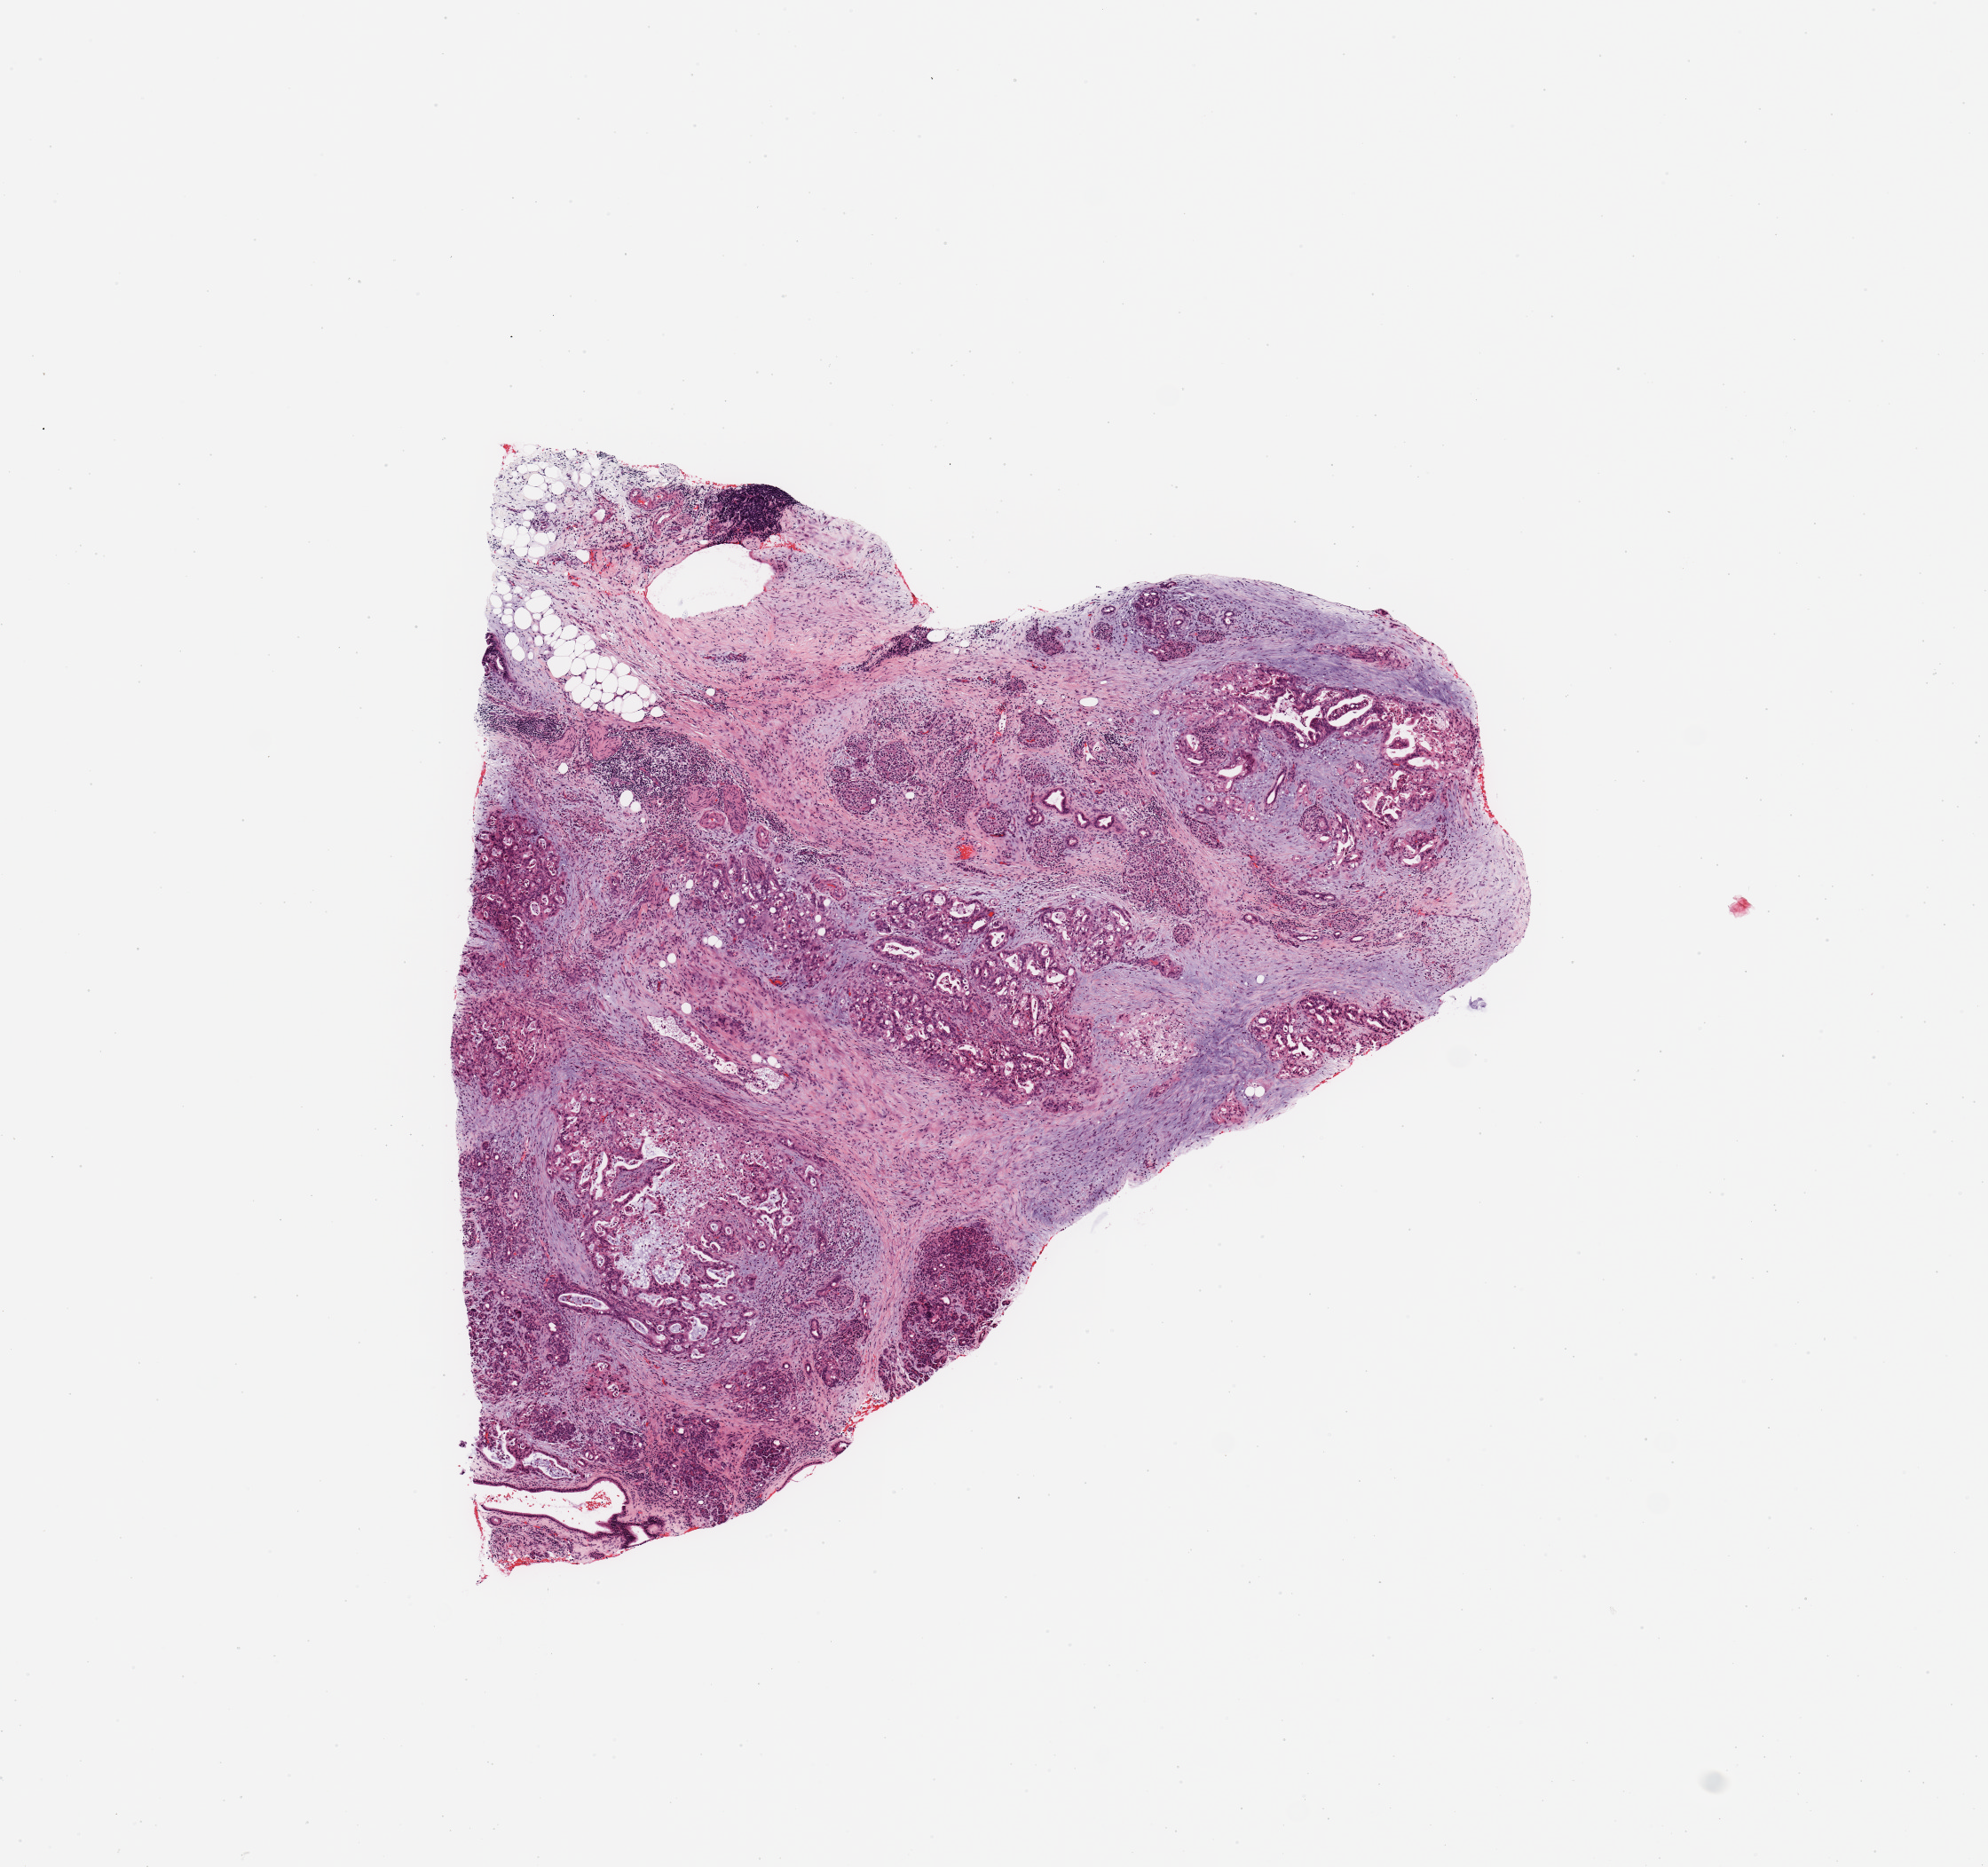
H&E-stained whole-slide image — shown as a low-resolution overview of the whole scanned area (about 8.9 x 8.3 mm). Pancreas, normal (non-tumour) tissue. 60-year-old female patient.
• this section: normal (non-tumour) tissue from the same patient
• patient diagnosis: Infiltrating duct carcinoma, NOS